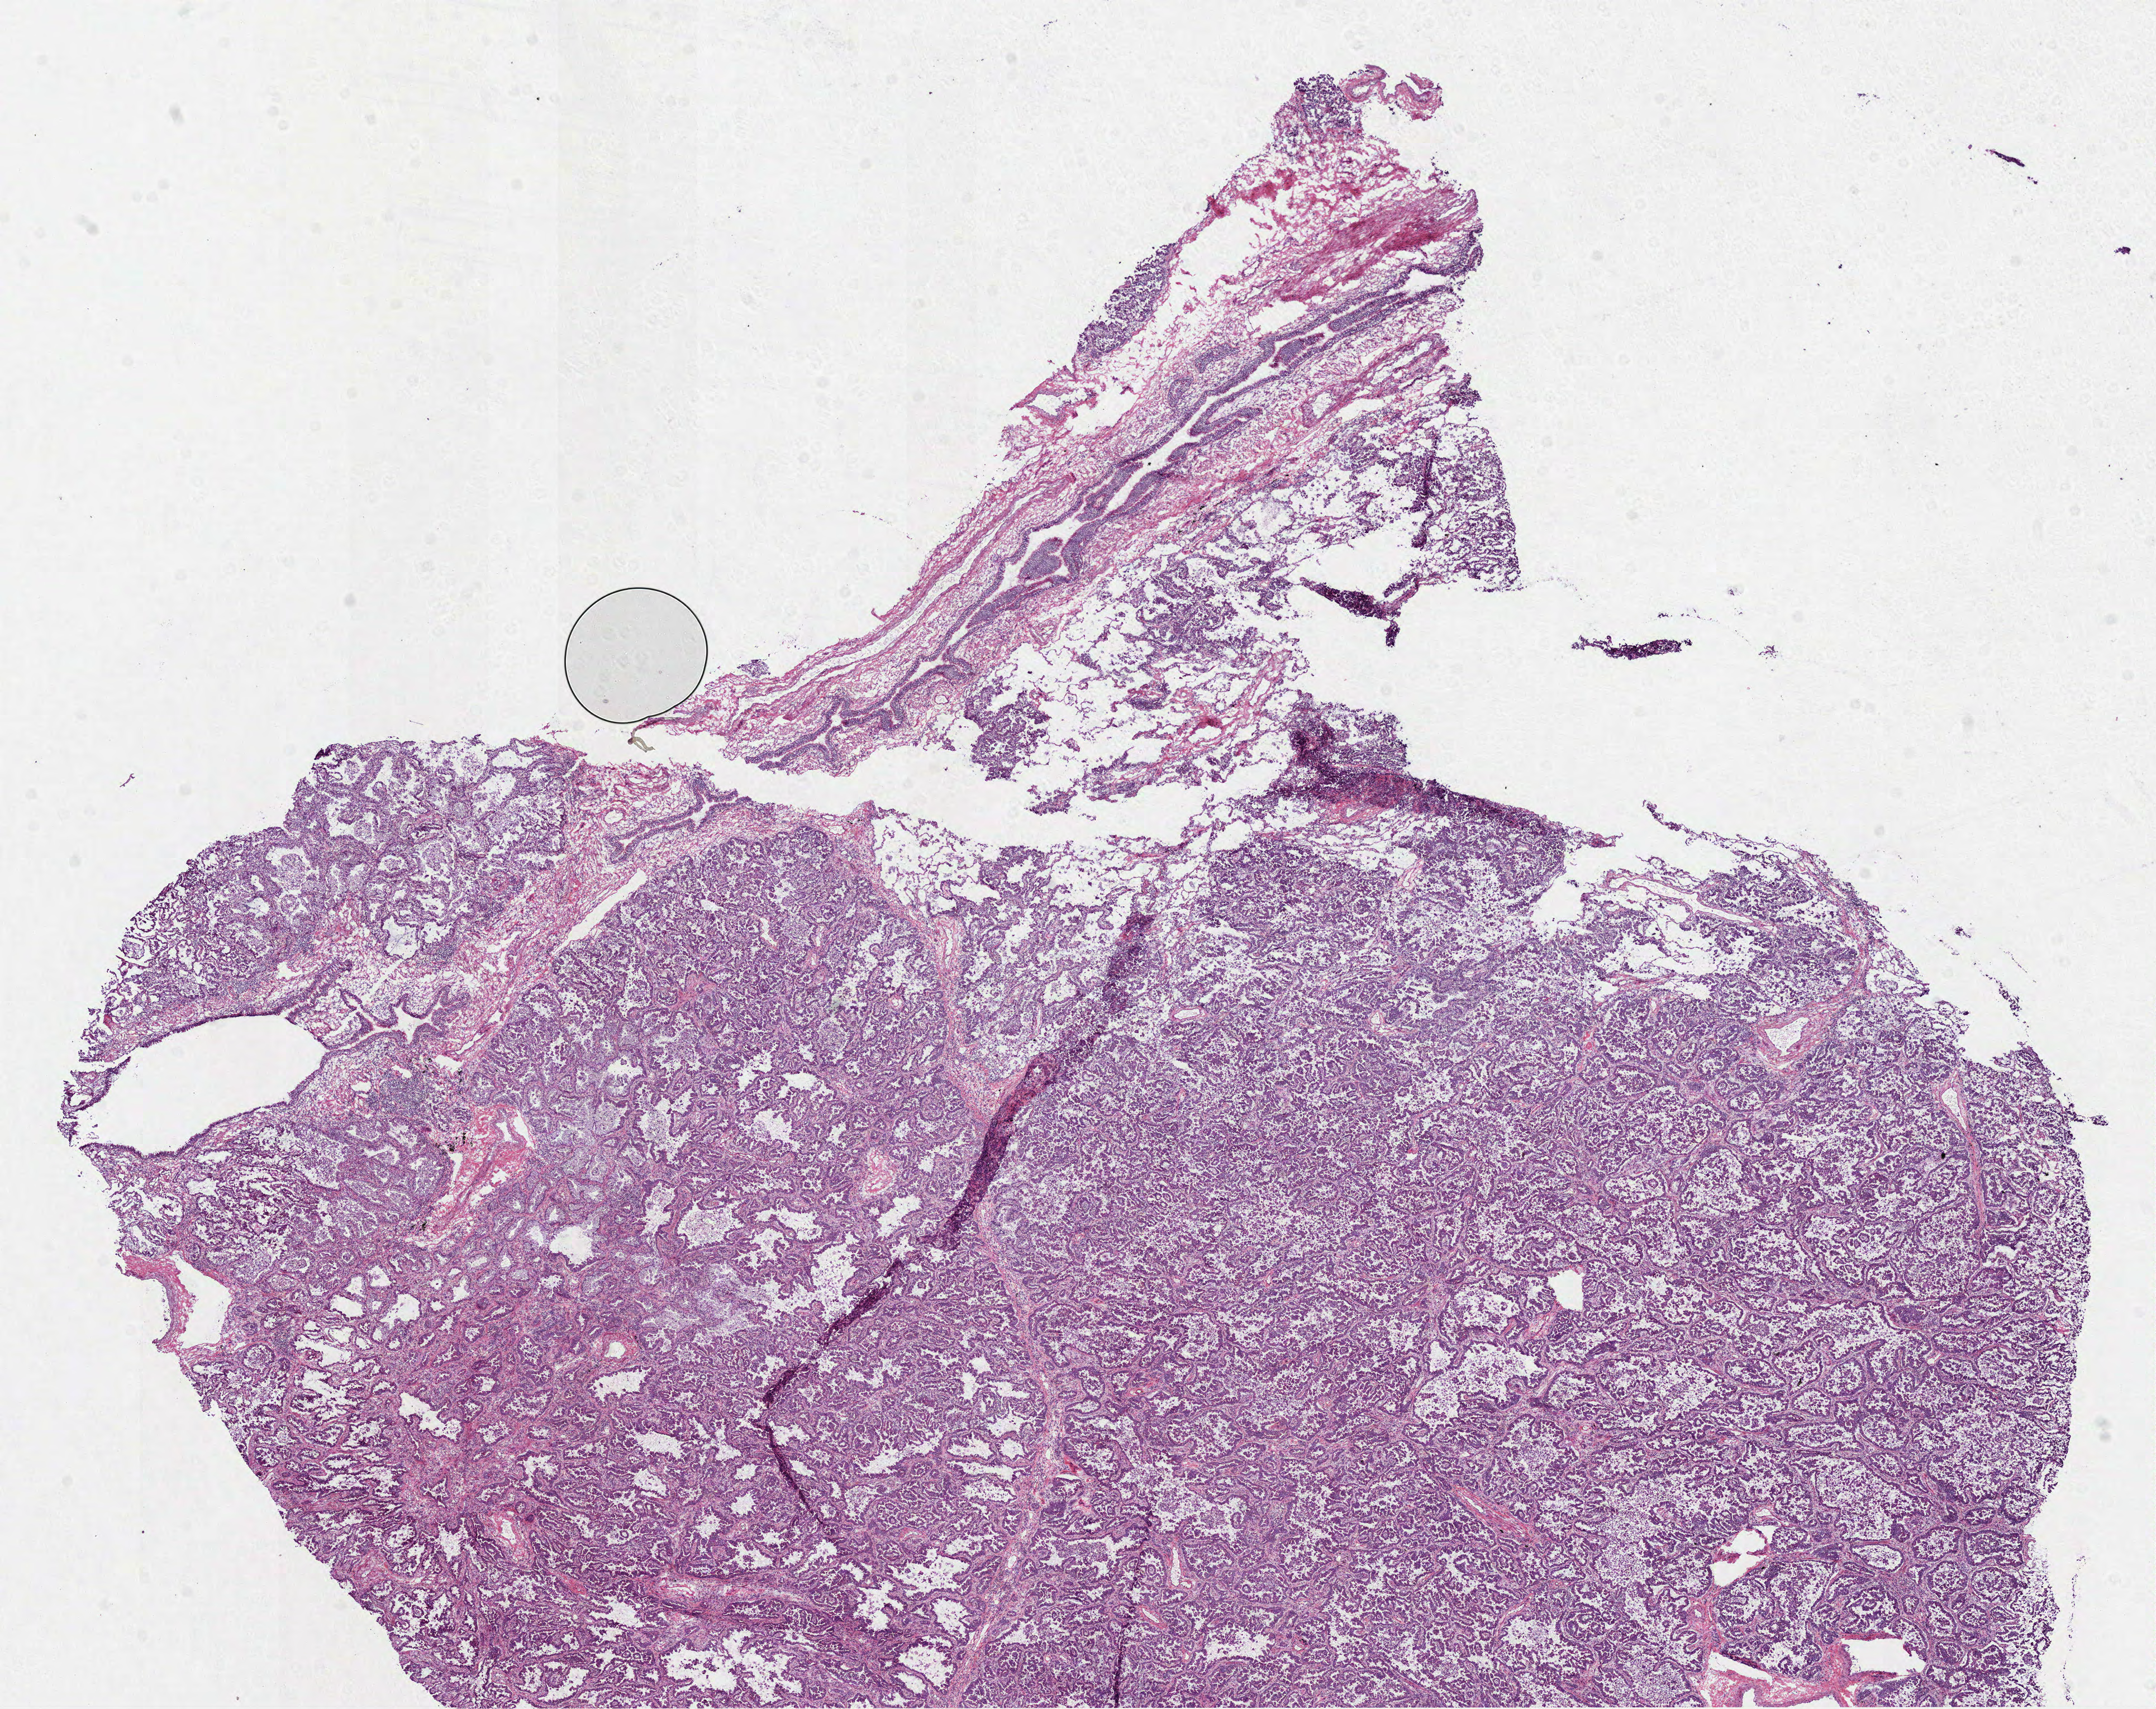
Whole-slide histology image, H&E-stained — whole scanned area (about 15.6 x 12.3 mm) shown as a low-resolution overview, frozen section from the bottom of the tissue portion, lung, primary tumour sample. Male patient; age at initial diagnosis 75 years. Composition of this section per pathologist review: tumour cells 85%, tumour nuclei 80%, normal cells 15%, stromal cells 0%, necrosis 0%. Inflammatory infiltration, as recorded: lymphocyte infiltration 10%, monocyte infiltration 5%, neutrophil infiltration 0%.
- laterality: right
- AJCC pathologic stage: IIB
- histologic diagnosis: Adenocarcinoma, NOS (upper lobe, lung)